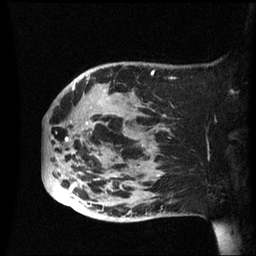
Breast MRI (dynamic contrast-enhanced), one sagittal slice. Slice 18 of 60 in the series (ordered by position). Dynamic contrast-enhanced series, image 2 of 3 at this slice position (ordered by acquisition). 1.5 T. TE 4.2 ms, TR 8.4 ms. 2.4 mm slice thickness. 256 × 256 image matrix, field of view 230 × 230 mm. Patient: female, 49 years.
Structures marked on this image (semi-automatic segmentation, software-assisted and operator-edited):
- analysis volume of interest (the breast-tissue region the enhancement analysis was run in; not a lesion): bounding box <42,62,174,222> (left, top, right, bottom; pixels)
- tumour enhancement mask (voxels above the 70 % enhancement threshold inside the analysis volume of interest): <65,137,103,220>